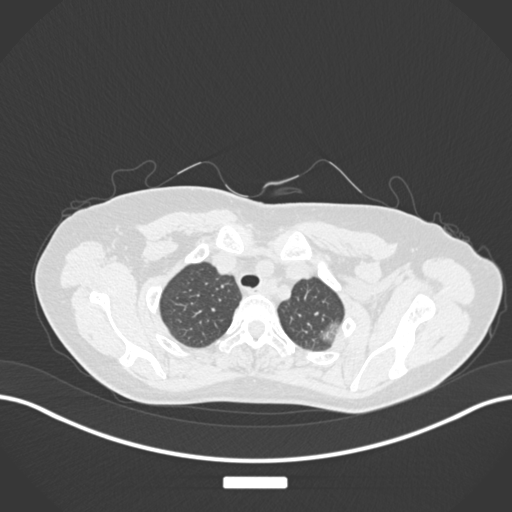
Chest CT, one axial slice; position 150 of 181 along the scan axis; reconstruction kernel B30f; 120 kVp; lung window (W 1500 / L -600 HU); 512 × 512 image matrix, field of view 400 × 400 mm. Patient: female, 58 years. Case-level facts recorded for this patient, not image findings: clinical TNM (as recorded): T1c N0 M0.
Outlined on this slice (bounding box drawn by a radiologist):
- lung tumour (recorded histology: adenocarcinoma): bounding box (x1, y1, x2, y2) in pixels: (319, 318, 344, 343)